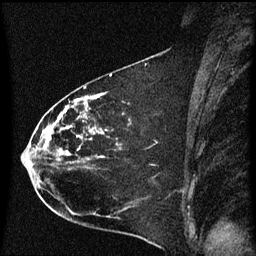
Breast MRI (dynamic contrast-enhanced), one sagittal slice. Position 32 of 60 along the scan axis. Dynamic contrast-enhanced series, image 2 of 3 at this slice position (ordered by acquisition). 1.5 T. TE 4.2 ms, TR 8.4 ms. 256 × 256 image matrix, field of view 200 × 200 mm. Female patient, age 35 years. Case-level facts recorded for this patient, not image findings: setting: breast cancer imaged before/during neoadjuvant chemotherapy; receptor status: HER2-positive.
Annotated regions visible in this slice (semi-automatic segmentation, software-assisted and operator-edited):
- analysis volume of interest (the breast-tissue region the enhancement analysis was run in; not a lesion): bounding box [x1, y1, x2, y2] px = [23, 68, 174, 173]
- tumour enhancement mask (voxels above the 70 % enhancement threshold inside the analysis volume of interest): [32, 94, 103, 161]